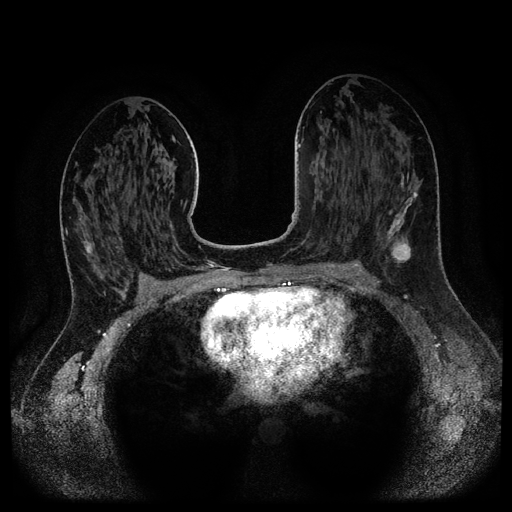
Breast MRI (dynamic contrast-enhanced, multi-phase), one axial slice. Dynamic contrast-enhanced series, time point 2 of 5 at this slice position (early post-contrast). 1.5 T. TE 2.6 ms, TR 5.3 ms. 512 × 512 image matrix, field of view 360 × 360 mm. Female patient, age 37 years.
Annotated regions visible in this slice (semi-automatic segmentation, software-assisted and operator-edited):
- breast lesion (labelled 'tumour' in the annotation; benign lesions carry a separate 'benign' label): box from (x=378, y=192) to (x=418, y=267) px